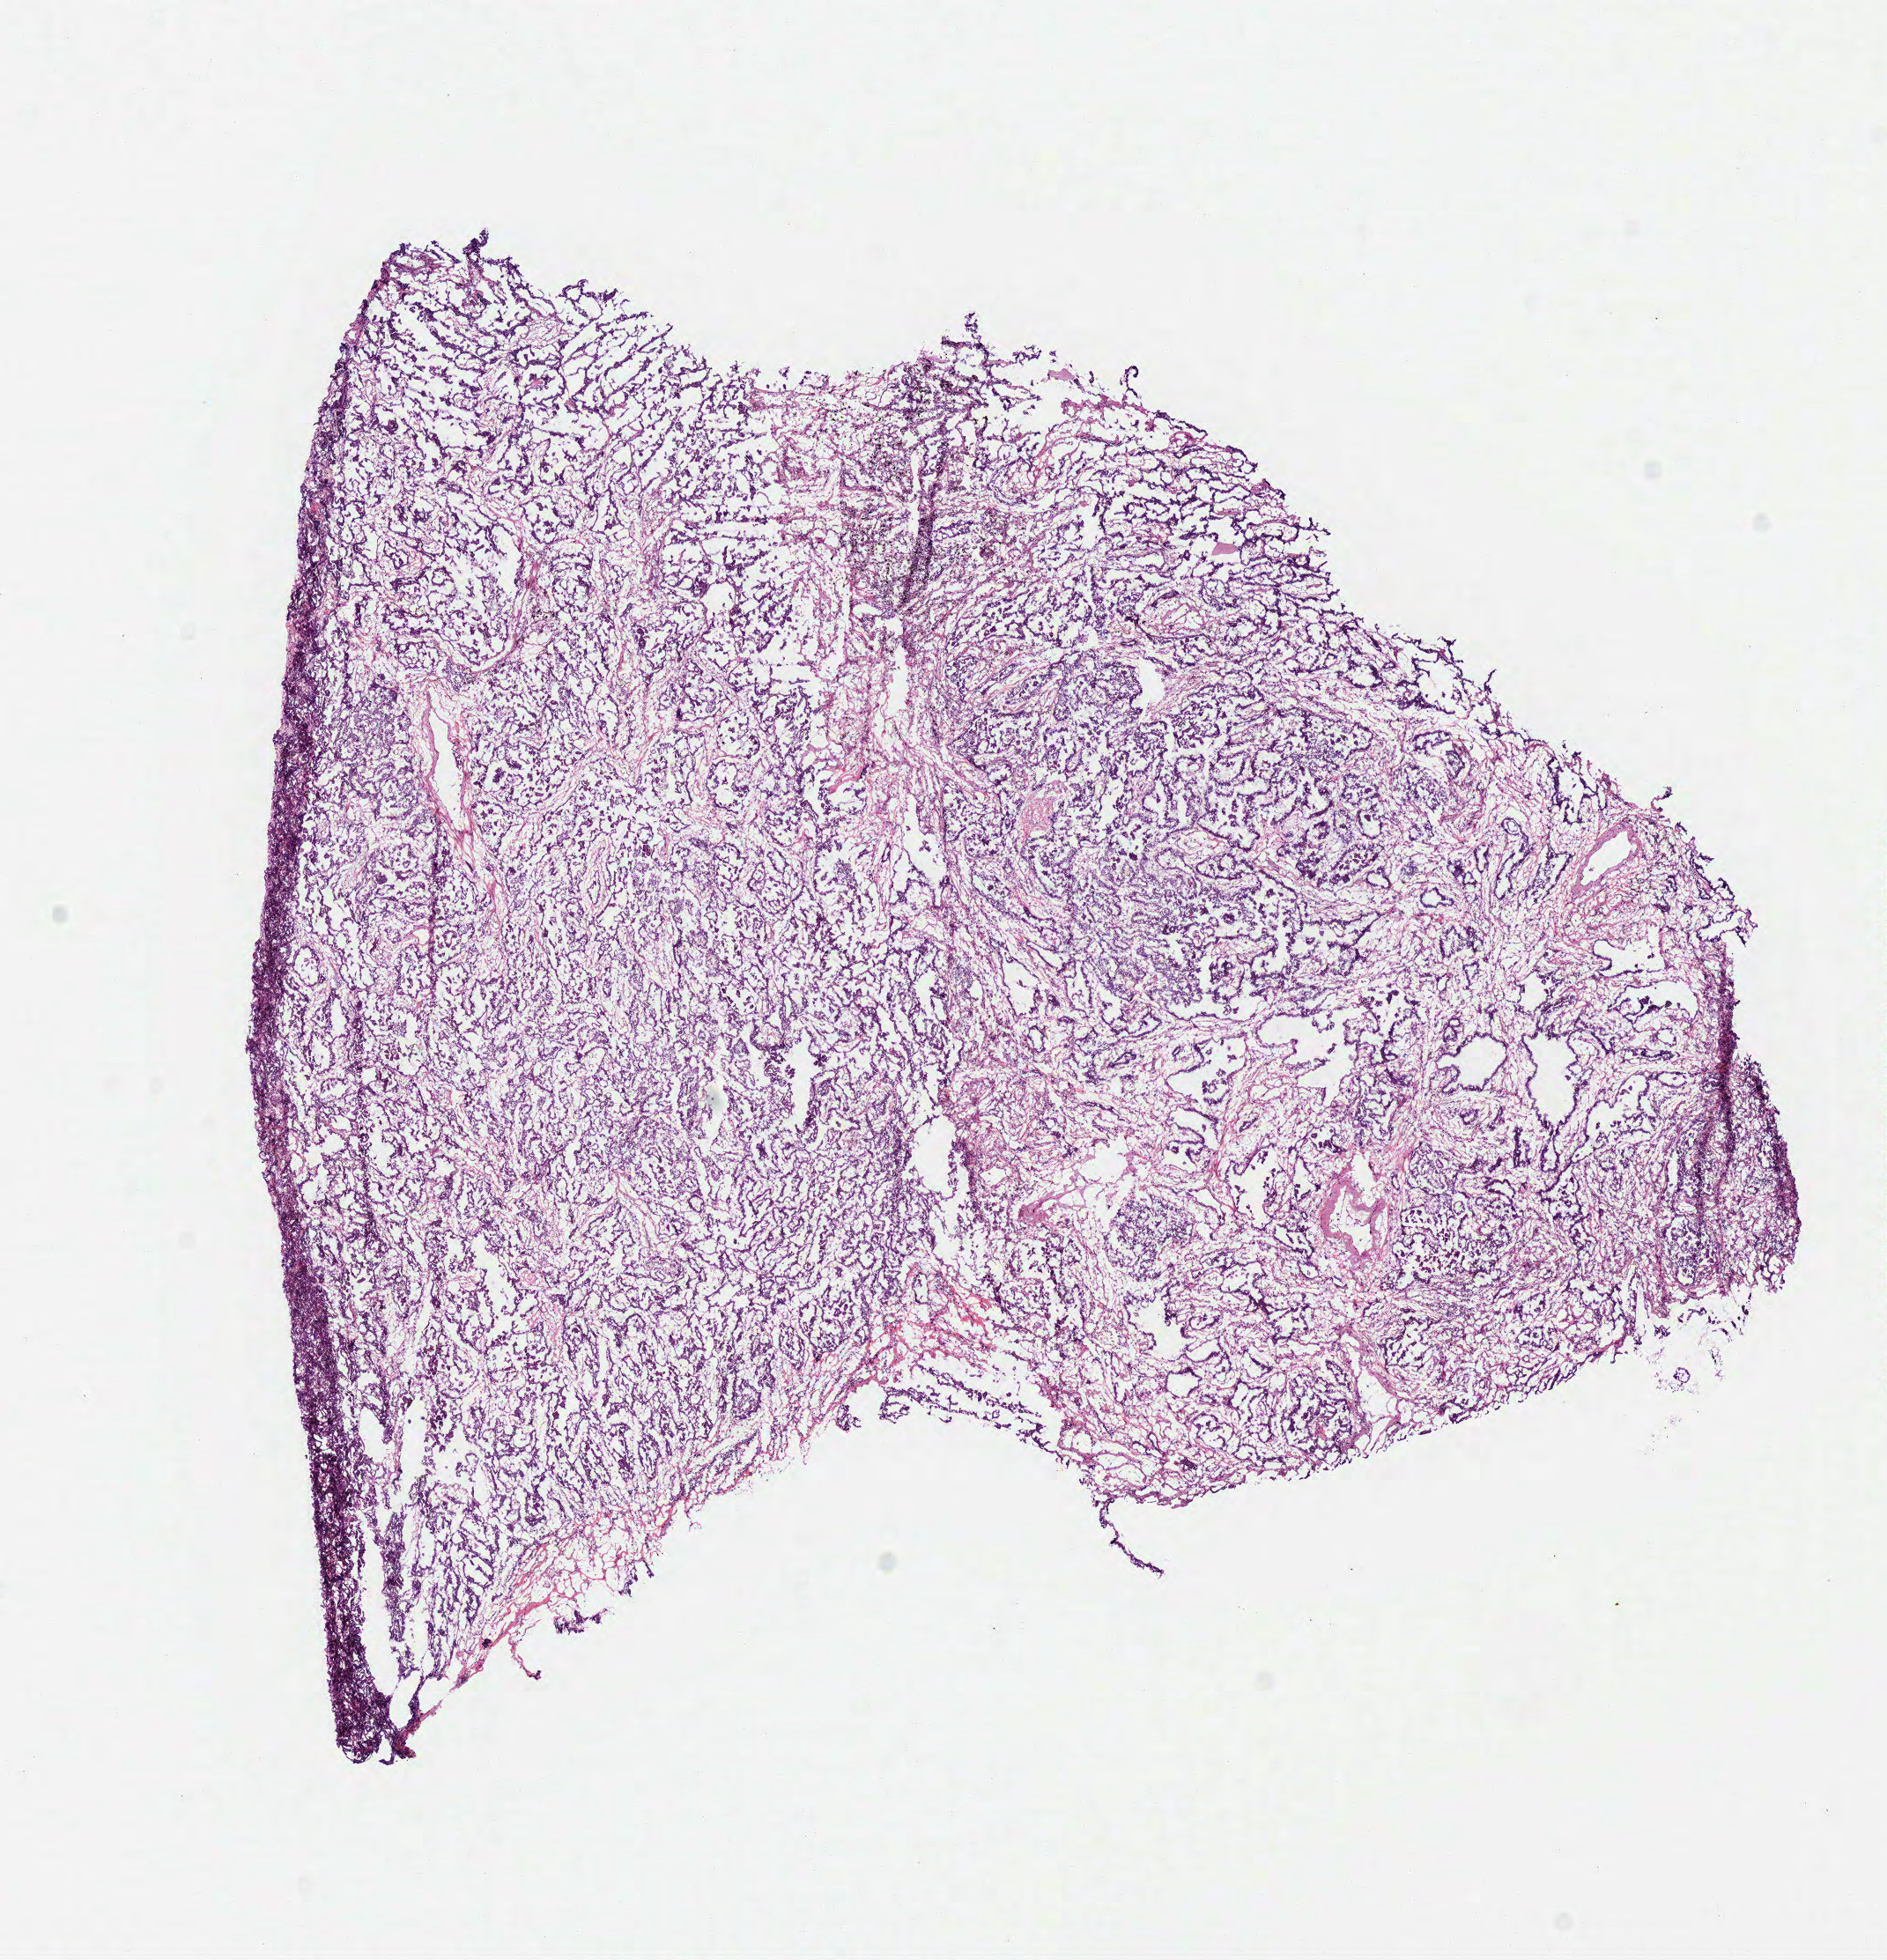
H&E whole-slide image, shown as a low-resolution overview of the whole scanned area (about 8.4 x 8.8 mm), frozen section, primary tumour sample from the lung. Female patient; age at initial diagnosis 59 years. Composition of this section per pathologist review: tumour cells 90%, tumour nuclei 80%, normal cells 0%, stromal cells 10%, necrosis 0%.
Pathologic diagnosis: Adenocarcinoma with mixed subtypes (lower lobe, lung). TNM: T4 N2 M0. AJCC pathologic stage: IIIB (6th edition).